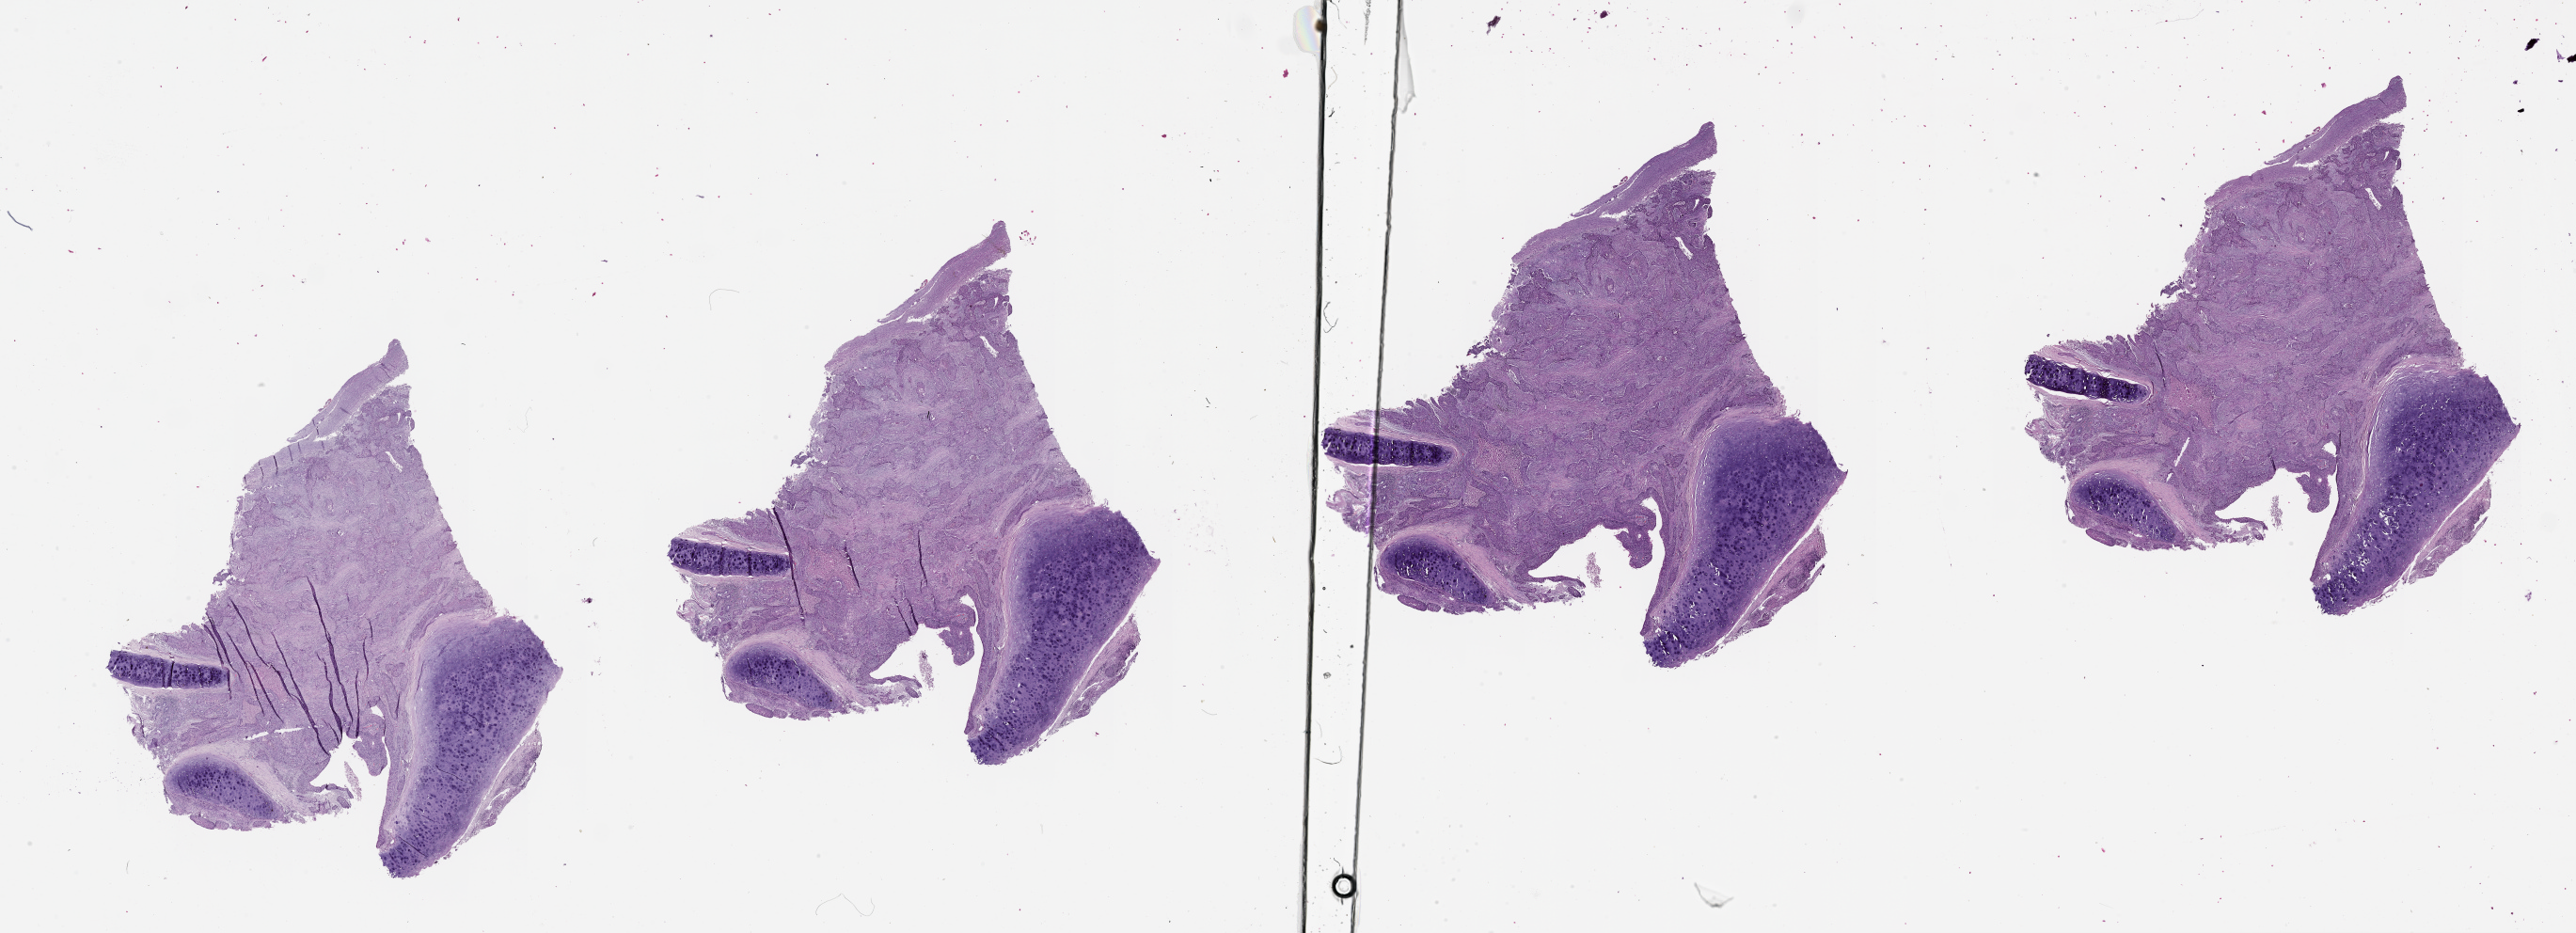
Digitized H&E tissue section (whole slide), low-resolution overview of the scanned area, about 44.1 x 16.0 mm (acquisition: 20x scan). Lung, tumour tissue. Male, 67 y/o.
Patient diagnosis (cohort enrolment): squamous cell carcinoma (lung).